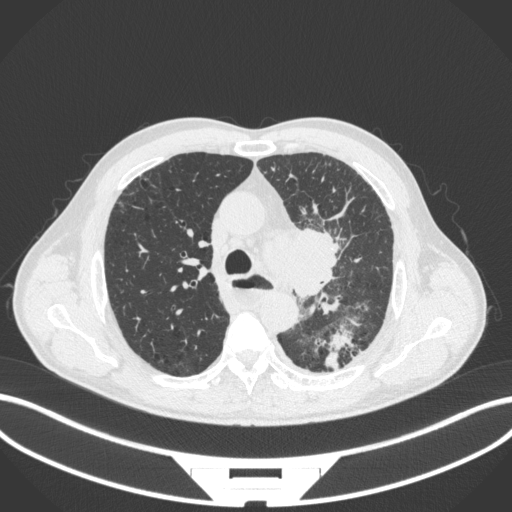
Chest CT, one axial slice; lung window (W 1500 / L -600 HU); 1 mm slice thickness; 512 × 512 image matrix. Male patient, age 57 years. From the clinical record (not read from this slice): clinical TNM (as recorded): T2a N1 M0.
Structures marked on this image (rectangle marked by the reading radiologist):
- lung tumour (recorded histology: squamous cell carcinoma): box from (x=258, y=218) to (x=348, y=303) px